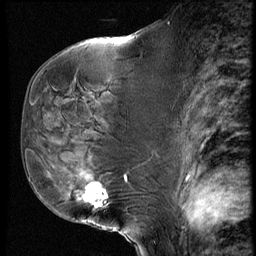
Breast MRI (dynamic contrast-enhanced), one sagittal slice. Position 31 of 60 along the scan axis. Dynamic contrast-enhanced series, image 2 of 4 at this slice position (ordered by acquisition). 1.5 T. TE 4.2 ms, TR 9 ms. 2.5 mm slice thickness. 256 × 256 image matrix, field of view 180 × 180 mm. Patient: female, 50 years. Case-level facts recorded for this patient, not image findings: setting: breast cancer imaged before/during neoadjuvant chemotherapy; receptor status: HR-positive, HER2-negative.
Outlined on this slice (semi-automatic segmentation, software-assisted and operator-edited):
- analysis volume of interest (the breast-tissue region the enhancement analysis was run in; not a lesion): bounding box [x1, y1, x2, y2] px = [48, 109, 135, 230]
- tumour enhancement mask (voxels above the 140 % enhancement threshold inside the analysis volume of interest): [84, 185, 108, 207]